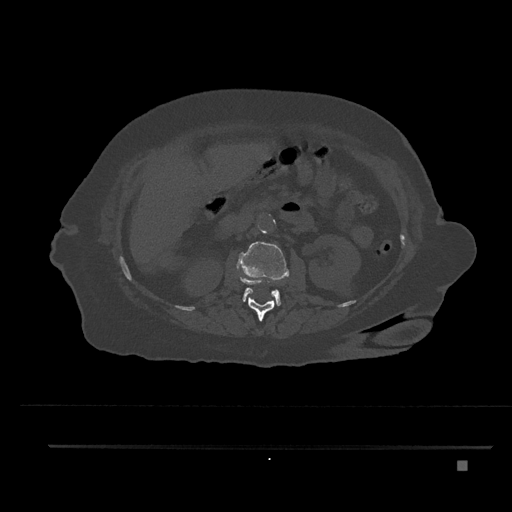
CT including the spine, one axial slice; position 204 of 797 along the scan axis; reconstruction kernel Br40s/3; 120 kVp; bone window (W 1800 / L 400 HU); 0.5 mm slice thickness; 512 × 512 image matrix, field of view 437 × 437 mm. Patient: female, 76 years. From the clinical record (not read from this slice): primary cancer: lung; vertebrae with lytic lesions (as recorded): T11, L3.
Structures marked on this image (semi-automatic segmentation, software-assisted and operator-edited):
- L1 vertebra: box from (x=237, y=277) to (x=276, y=321) px
- L2 vertebra: (x=237, y=242)–(x=290, y=305)